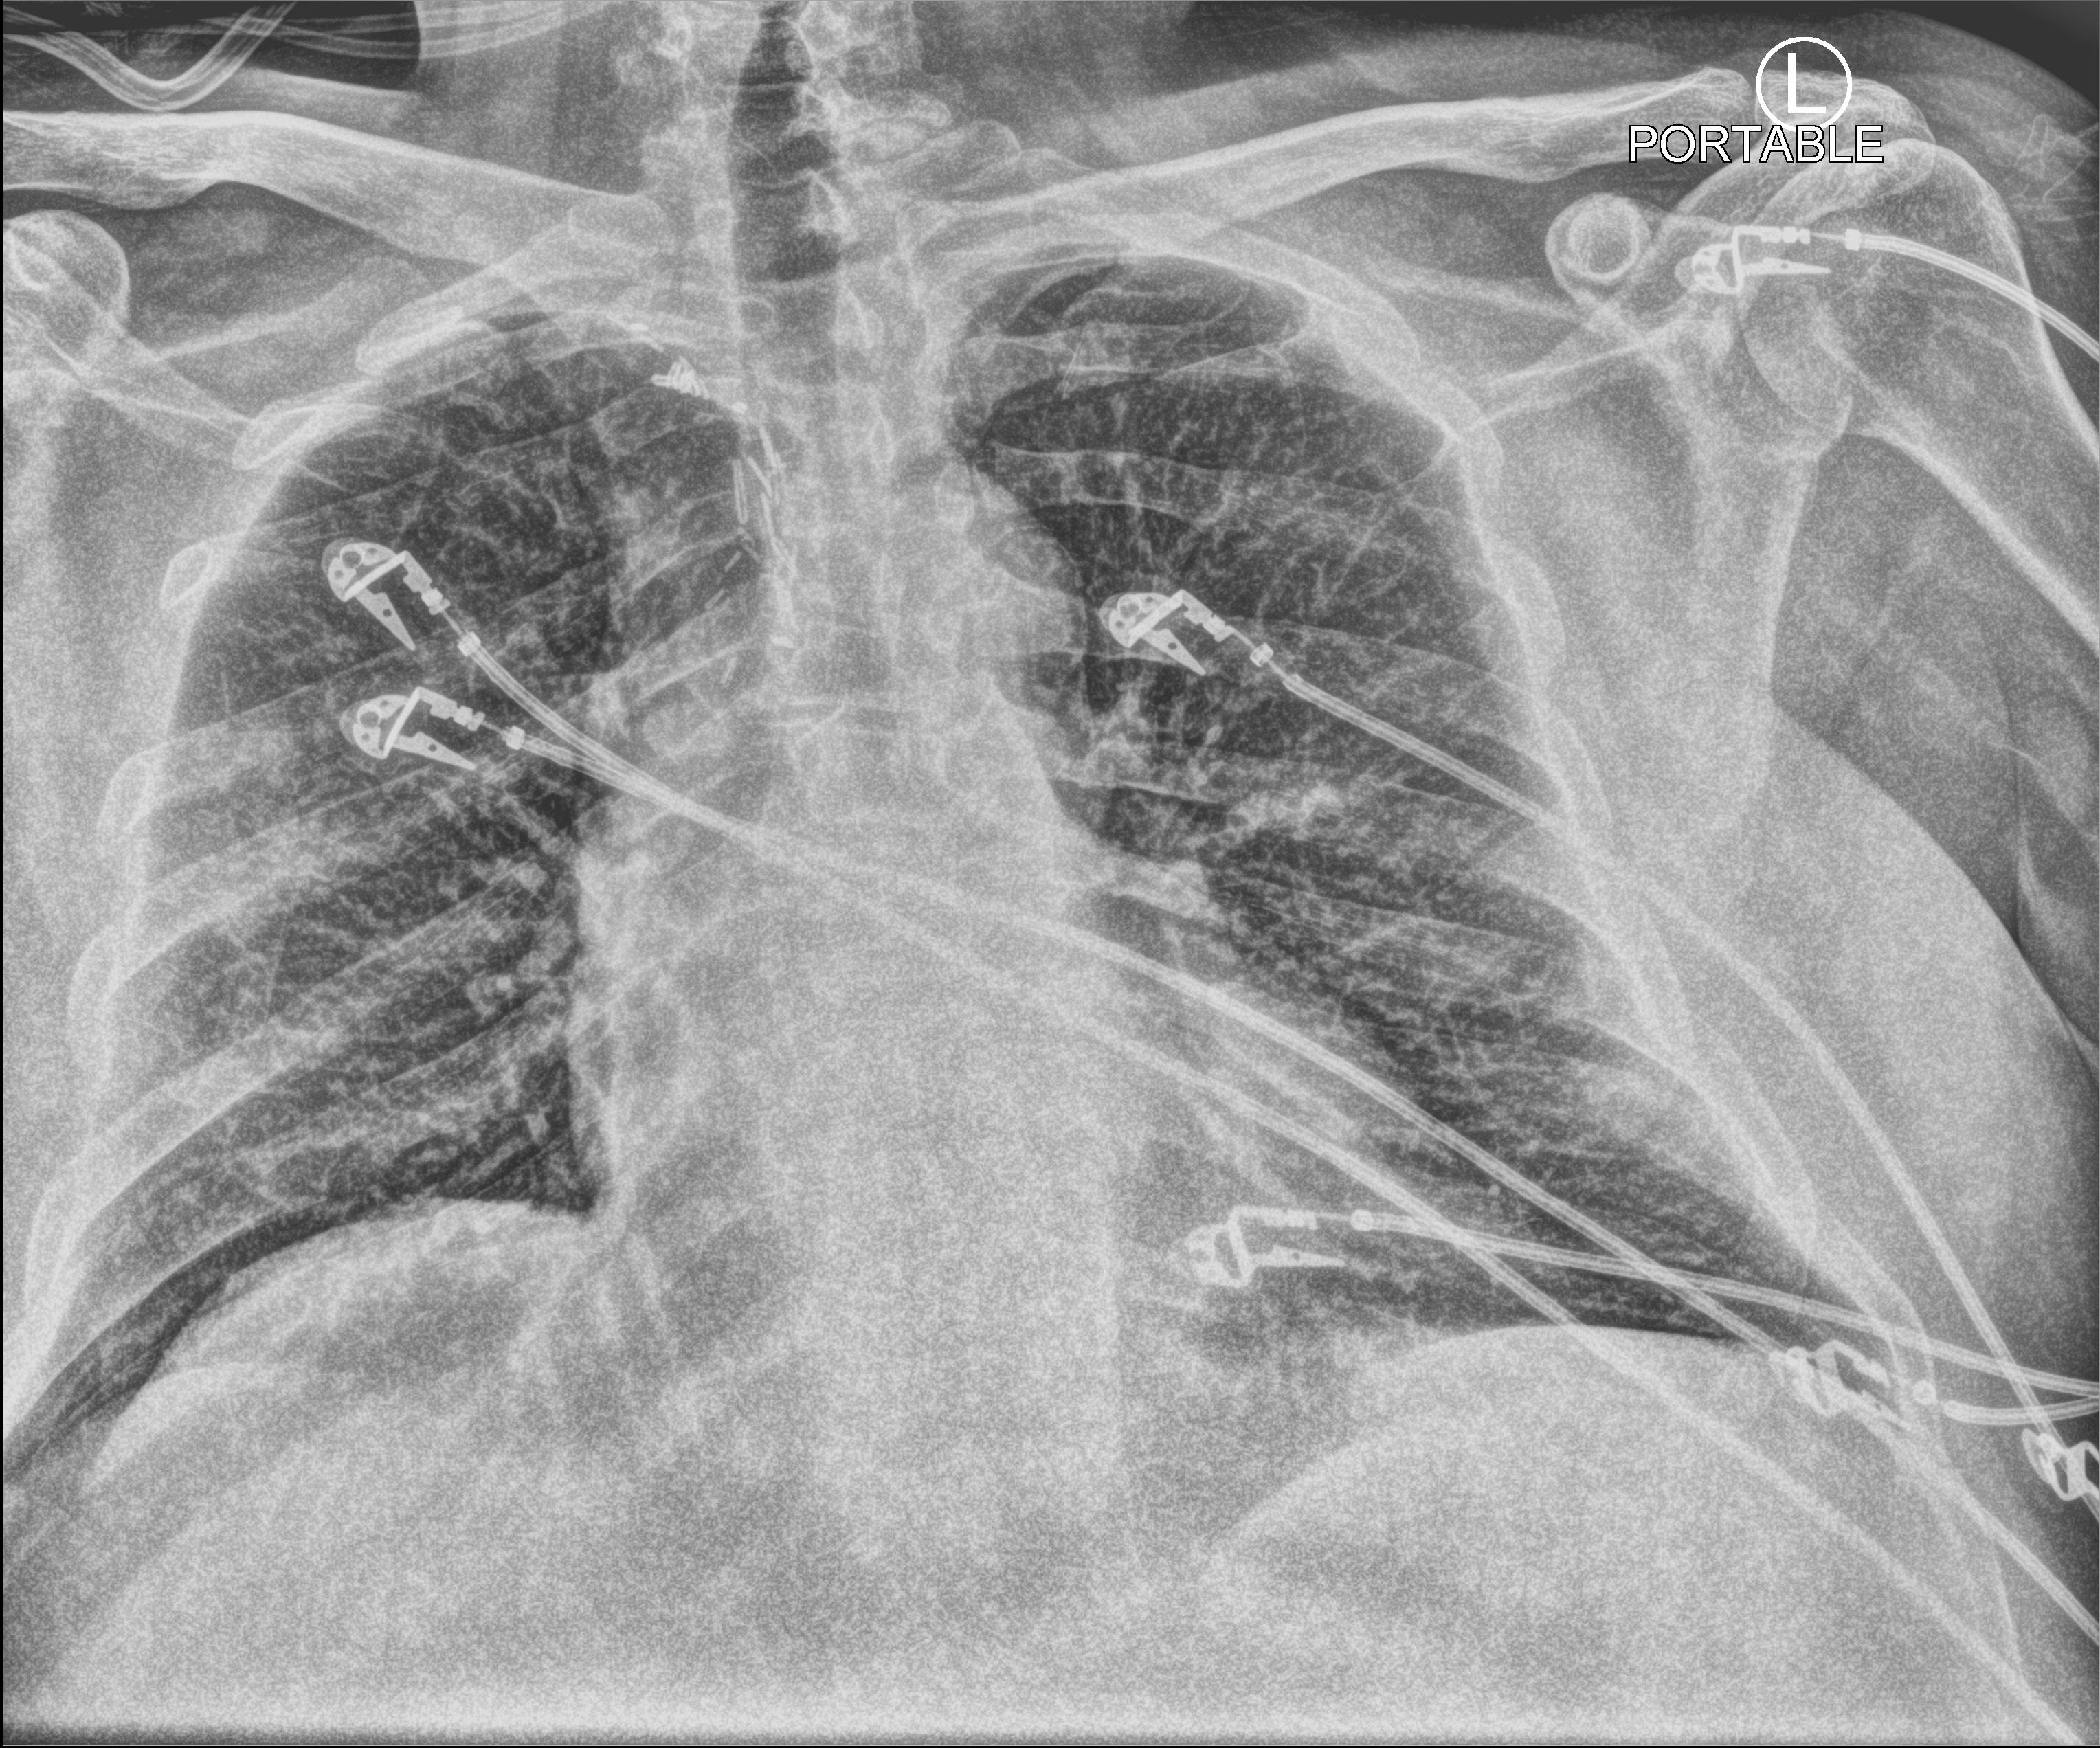
Portable chest radiograph, anteroposterior (AP) projection. Patient hospitalised with COVID-19, aged 18–59 years.
From the hospital-stay record, not from the radiograph (when in the stay this image was taken is not recorded): admitted to intensive care during this hospital stay: yes; length of hospital stay: 2 days; mechanically ventilated during this hospital stay: yes.